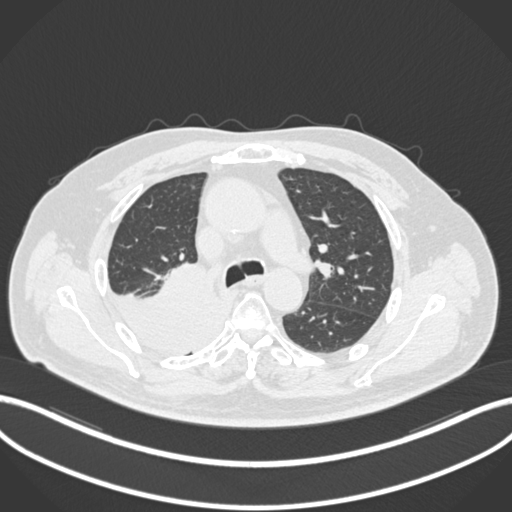
Chest CT, one axial slice. Position 134 of 218 along the scan axis. Reconstruction kernel B30f. 120 kVp. Lung window (W 1500 / L -600 HU). 1 mm slice thickness. 512 × 512 image matrix. Patient: male, 68 years. Case-level facts recorded for this patient, not image findings: clinical TNM (as recorded): T2a N0 M0.
Structures marked on this image (bounding box drawn by a radiologist):
- lung tumour (recorded histology: adenocarcinoma): bounding box (x1, y1, x2, y2) in pixels: (111, 260, 230, 355)